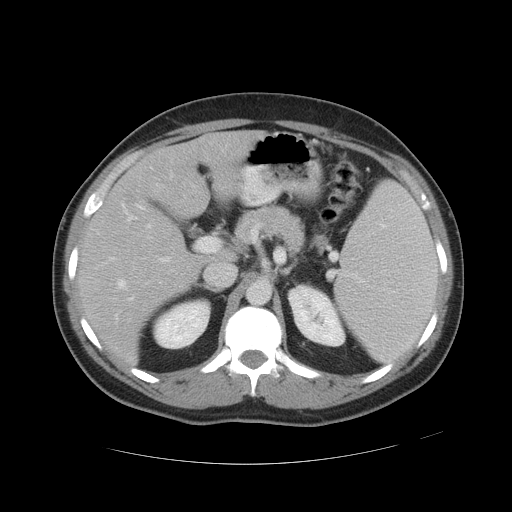
Contrast-enhanced abdominal CT, one axial slice; intravenous contrast given; soft-tissue window (W 400 / L 40 HU); 5 mm slice thickness; 512 × 512 image matrix, field of view 422 × 422 mm. Male patient, age 42 years. From the clinical record (not read from this slice): diagnosis: colorectal cancer liver metastases, imaged before liver resection; multiple liver metastases: yes; largest metastasis: 2.8 cm; chemotherapy before resection: yes.
Outlined on this slice (manually delineated by an expert):
- hepatic veins: box from (x=119, y=204) to (x=154, y=289) px
- liver: (x=79, y=133)–(x=246, y=360)
- planned liver remnant (the part of the liver to remain after resection): (x=79, y=133)–(x=246, y=360)
- portal vein (with intrahepatic branches): (x=144, y=238)–(x=215, y=262)
- liver metastasis: (x=125, y=191)–(x=132, y=200)